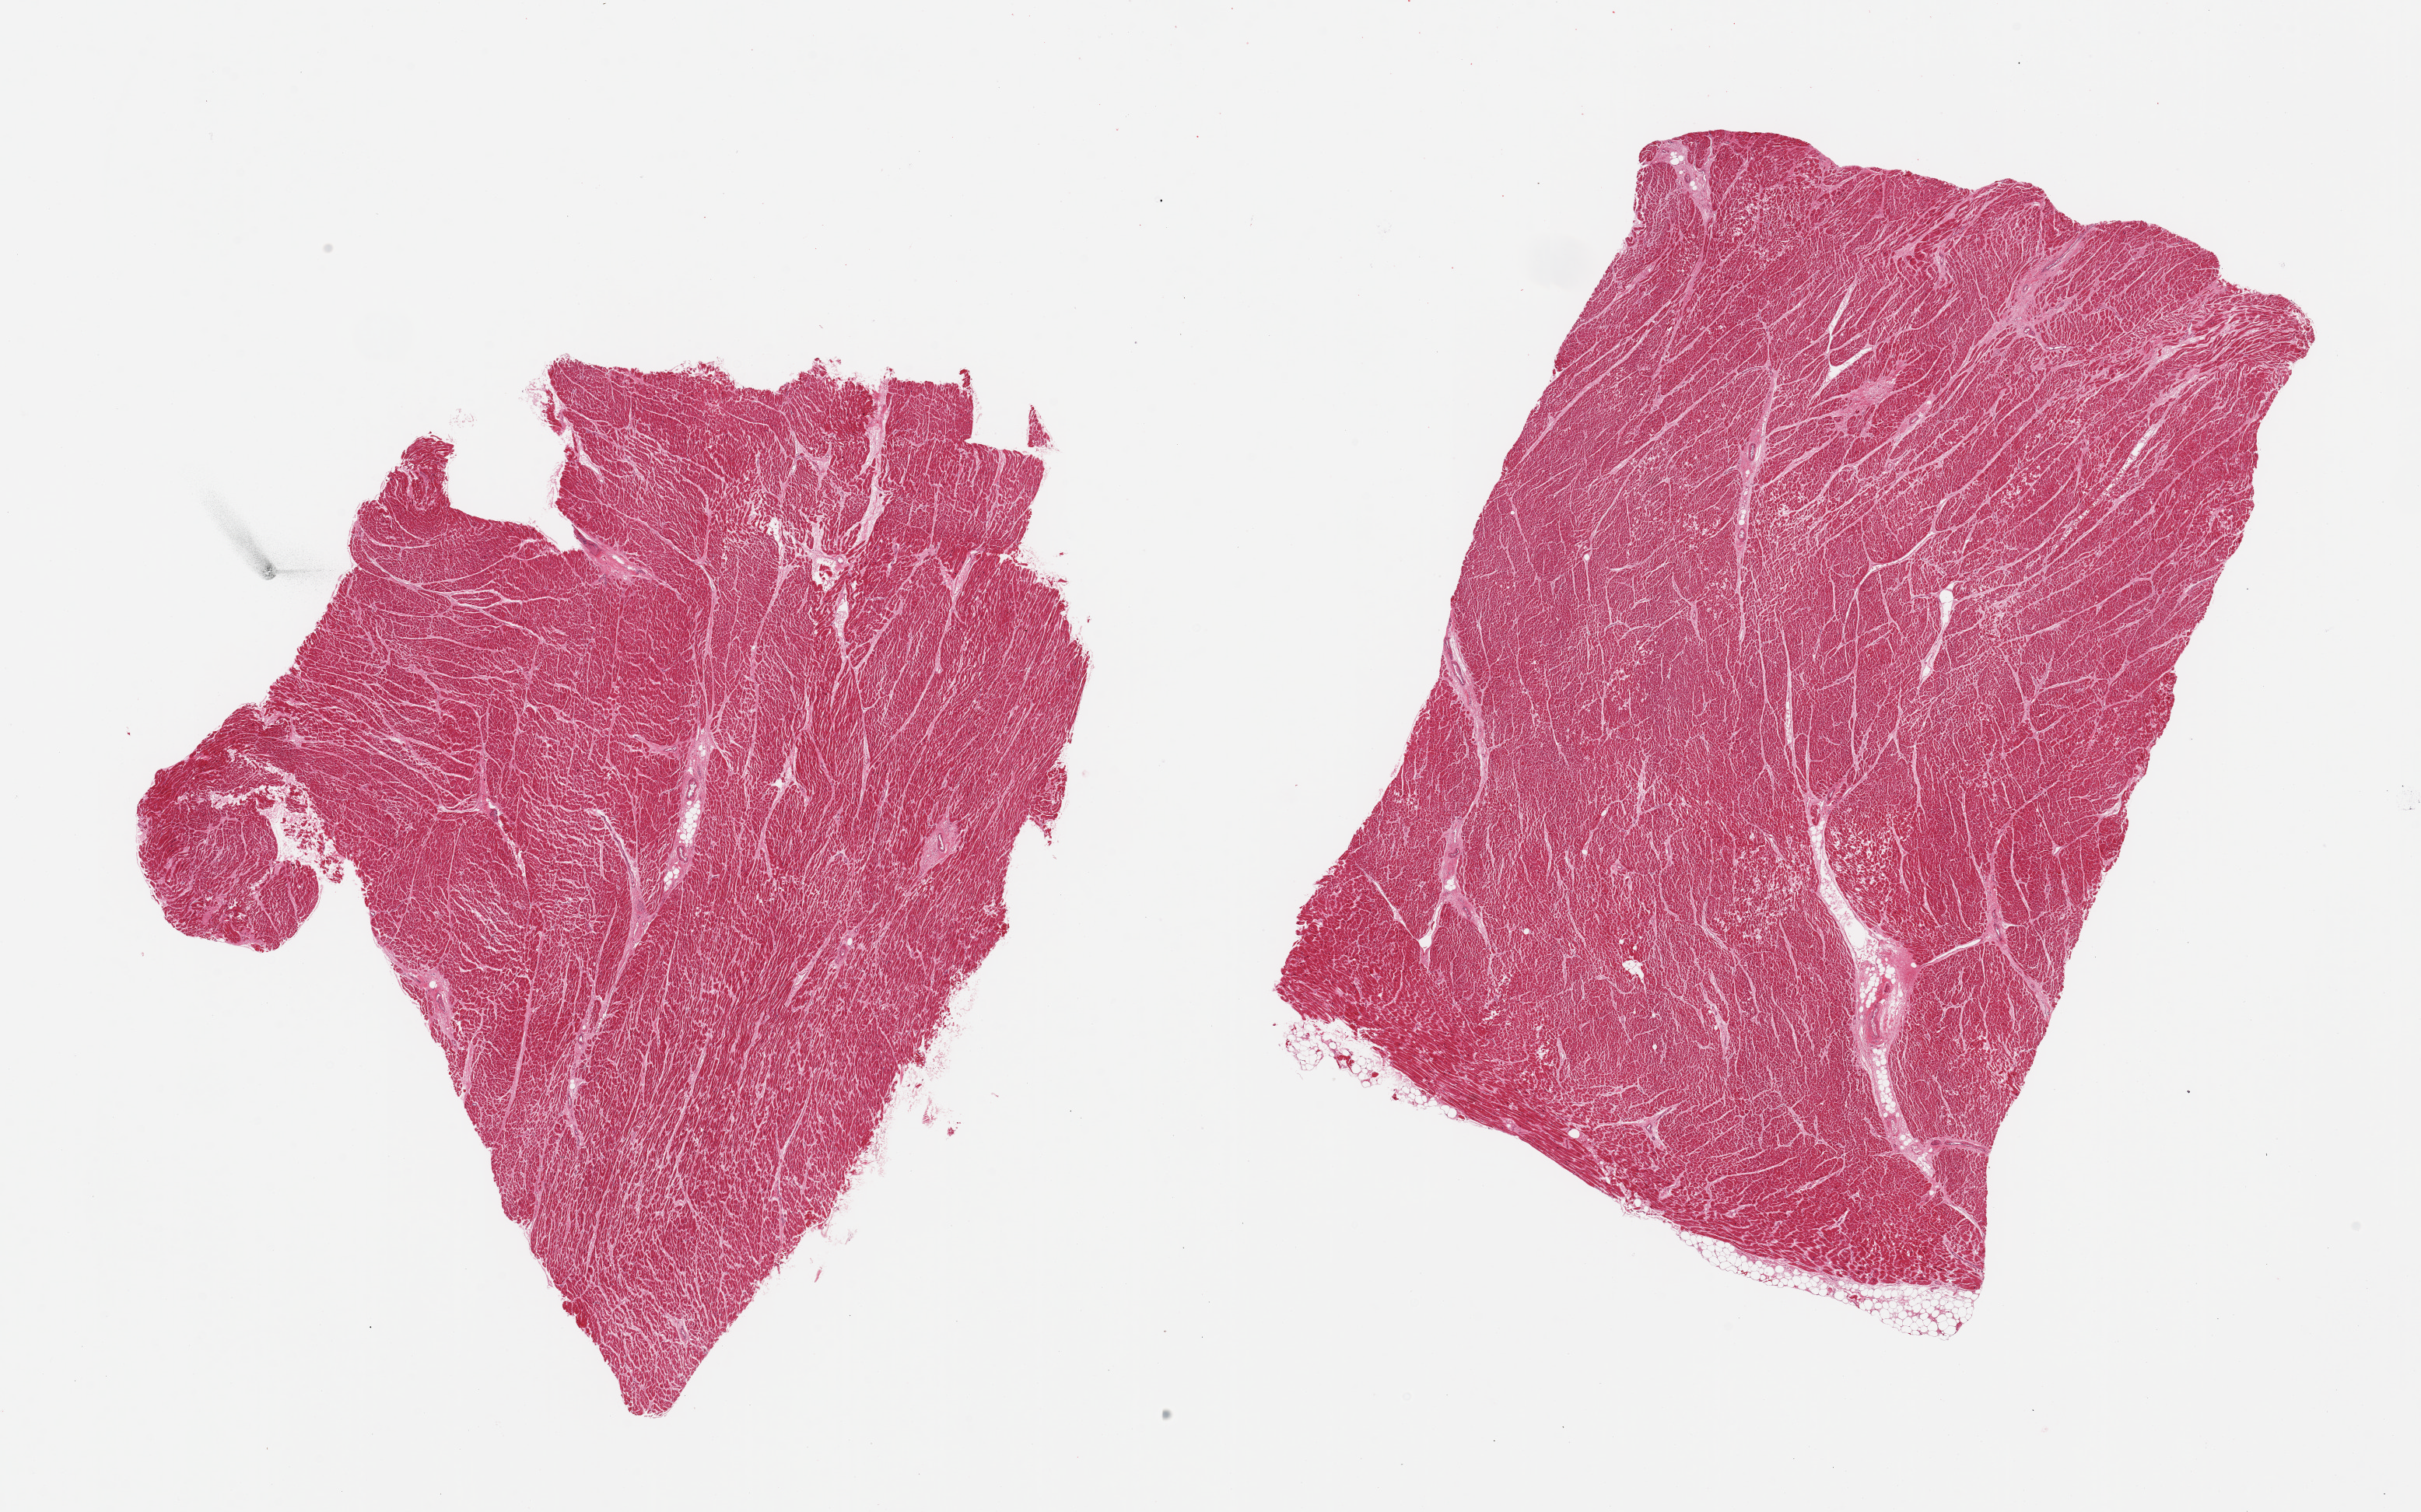
Digitized H&E-stained section — whole scanned area (about 24.6 x 15.4 mm) shown as a low-resolution overview. PAXgene-fixed paraffin-embedded (PFPE) section. Target tissue: heart. Donor tissue sample. Donor sex: male.
Review note (as recorded): 2 pieces; accentuation of interstitial component.